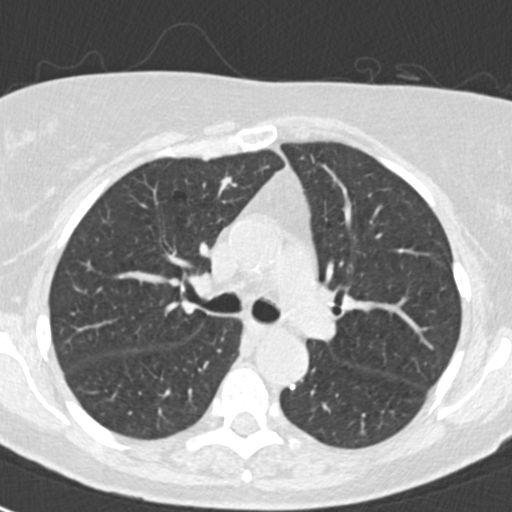
Low-dose screening chest CT, axial slice, baseline annual screen, lung window (W 1500 / L -600 HU), 2 mm slice thickness, standard (soft-tissue) reconstruction kernel (B30f). Female participant, aged 72 years at enrolment. Former smoker at enrolment.
Lesion marked by an expert reader, box from (x=199, y=166) to (x=246, y=207) px. No non-calcified nodule or mass ≥4 mm was recorded by the screening reader at this exam. Official screen result: negative screen, no significant abnormalities. Later outcome: lung cancer diagnosed 828 days after this screen (after the third annual screen) — adenocarcinoma, NOS, right upper lobe, moderately differentiated (G2), stage IA (AJCC 6th edition), 15 mm at pathology.